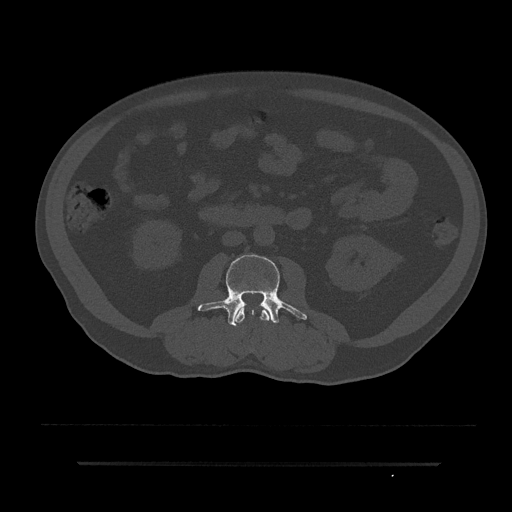
CT including the spine, one axial slice. Position 21 of 797 along the scan axis. 120 kVp. Bone window (W 1800 / L 400 HU). 0.5 mm slice thickness. 512 × 512 image matrix. Patient: male, 59 years. From the clinical record (not read from this slice): primary cancer: bile ducts.
Structures marked on this image (semi-automatic segmentation, software-assisted and operator-edited):
- L2 vertebra: bounding box (x1, y1, x2, y2) in pixels: (234, 306, 271, 324)
- L3 vertebra: (198, 254, 307, 326)